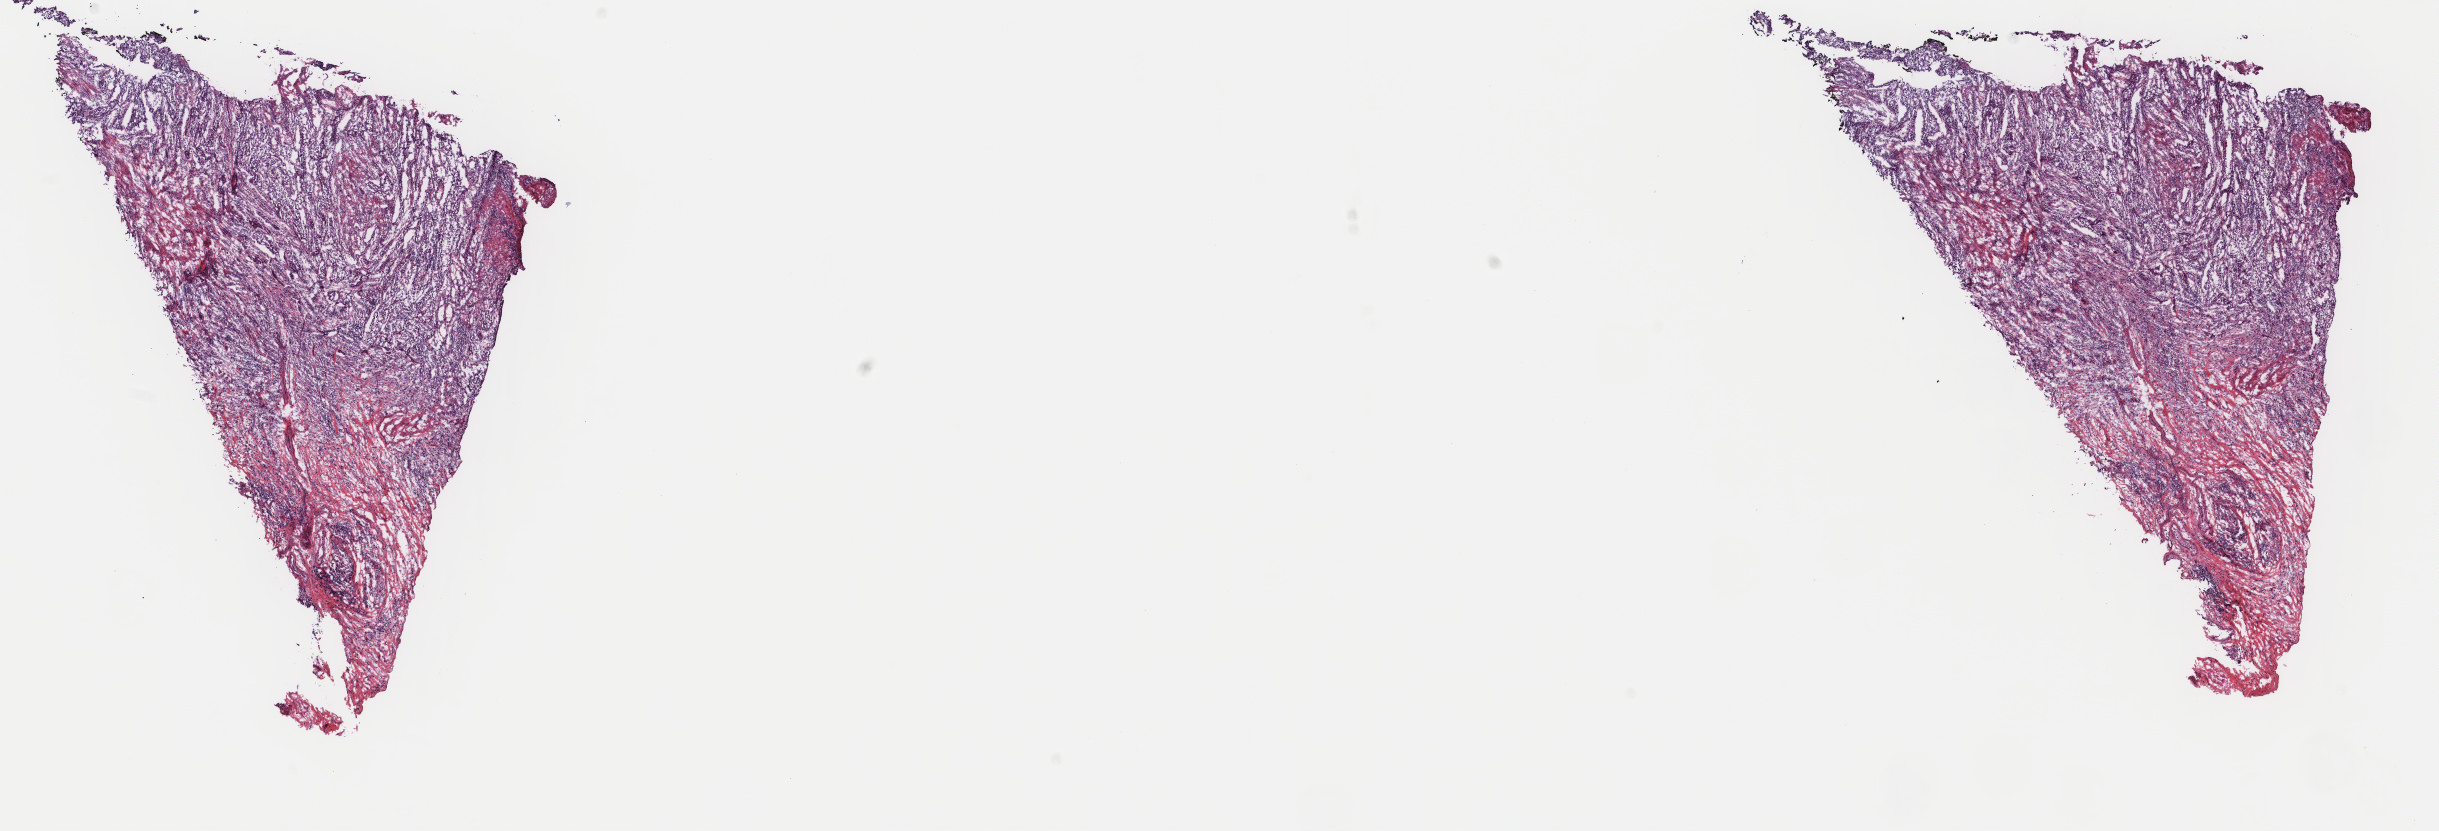
H&E whole-slide image, low-resolution overview of the scanned area, about 19.4 x 6.6 mm (from a 40x scan), frozen section from the top of the tissue portion, primary tumour sample from the bladder. Male, age 66 years at initial diagnosis. Histologic grade: high grade. Composition of this section per pathologist review: tumour cells 60%, tumour nuclei 70%, normal cells 0%, stromal cells 40%, necrosis 0%. Inflammatory infiltration, as recorded: lymphocyte infiltration 0%, monocyte infiltration 0%, neutrophil infiltration 0%.
- AJCC pathologic stage: II (7th edition)
- histologic diagnosis: Transitional cell carcinoma
- TNM: T2b N0 MX